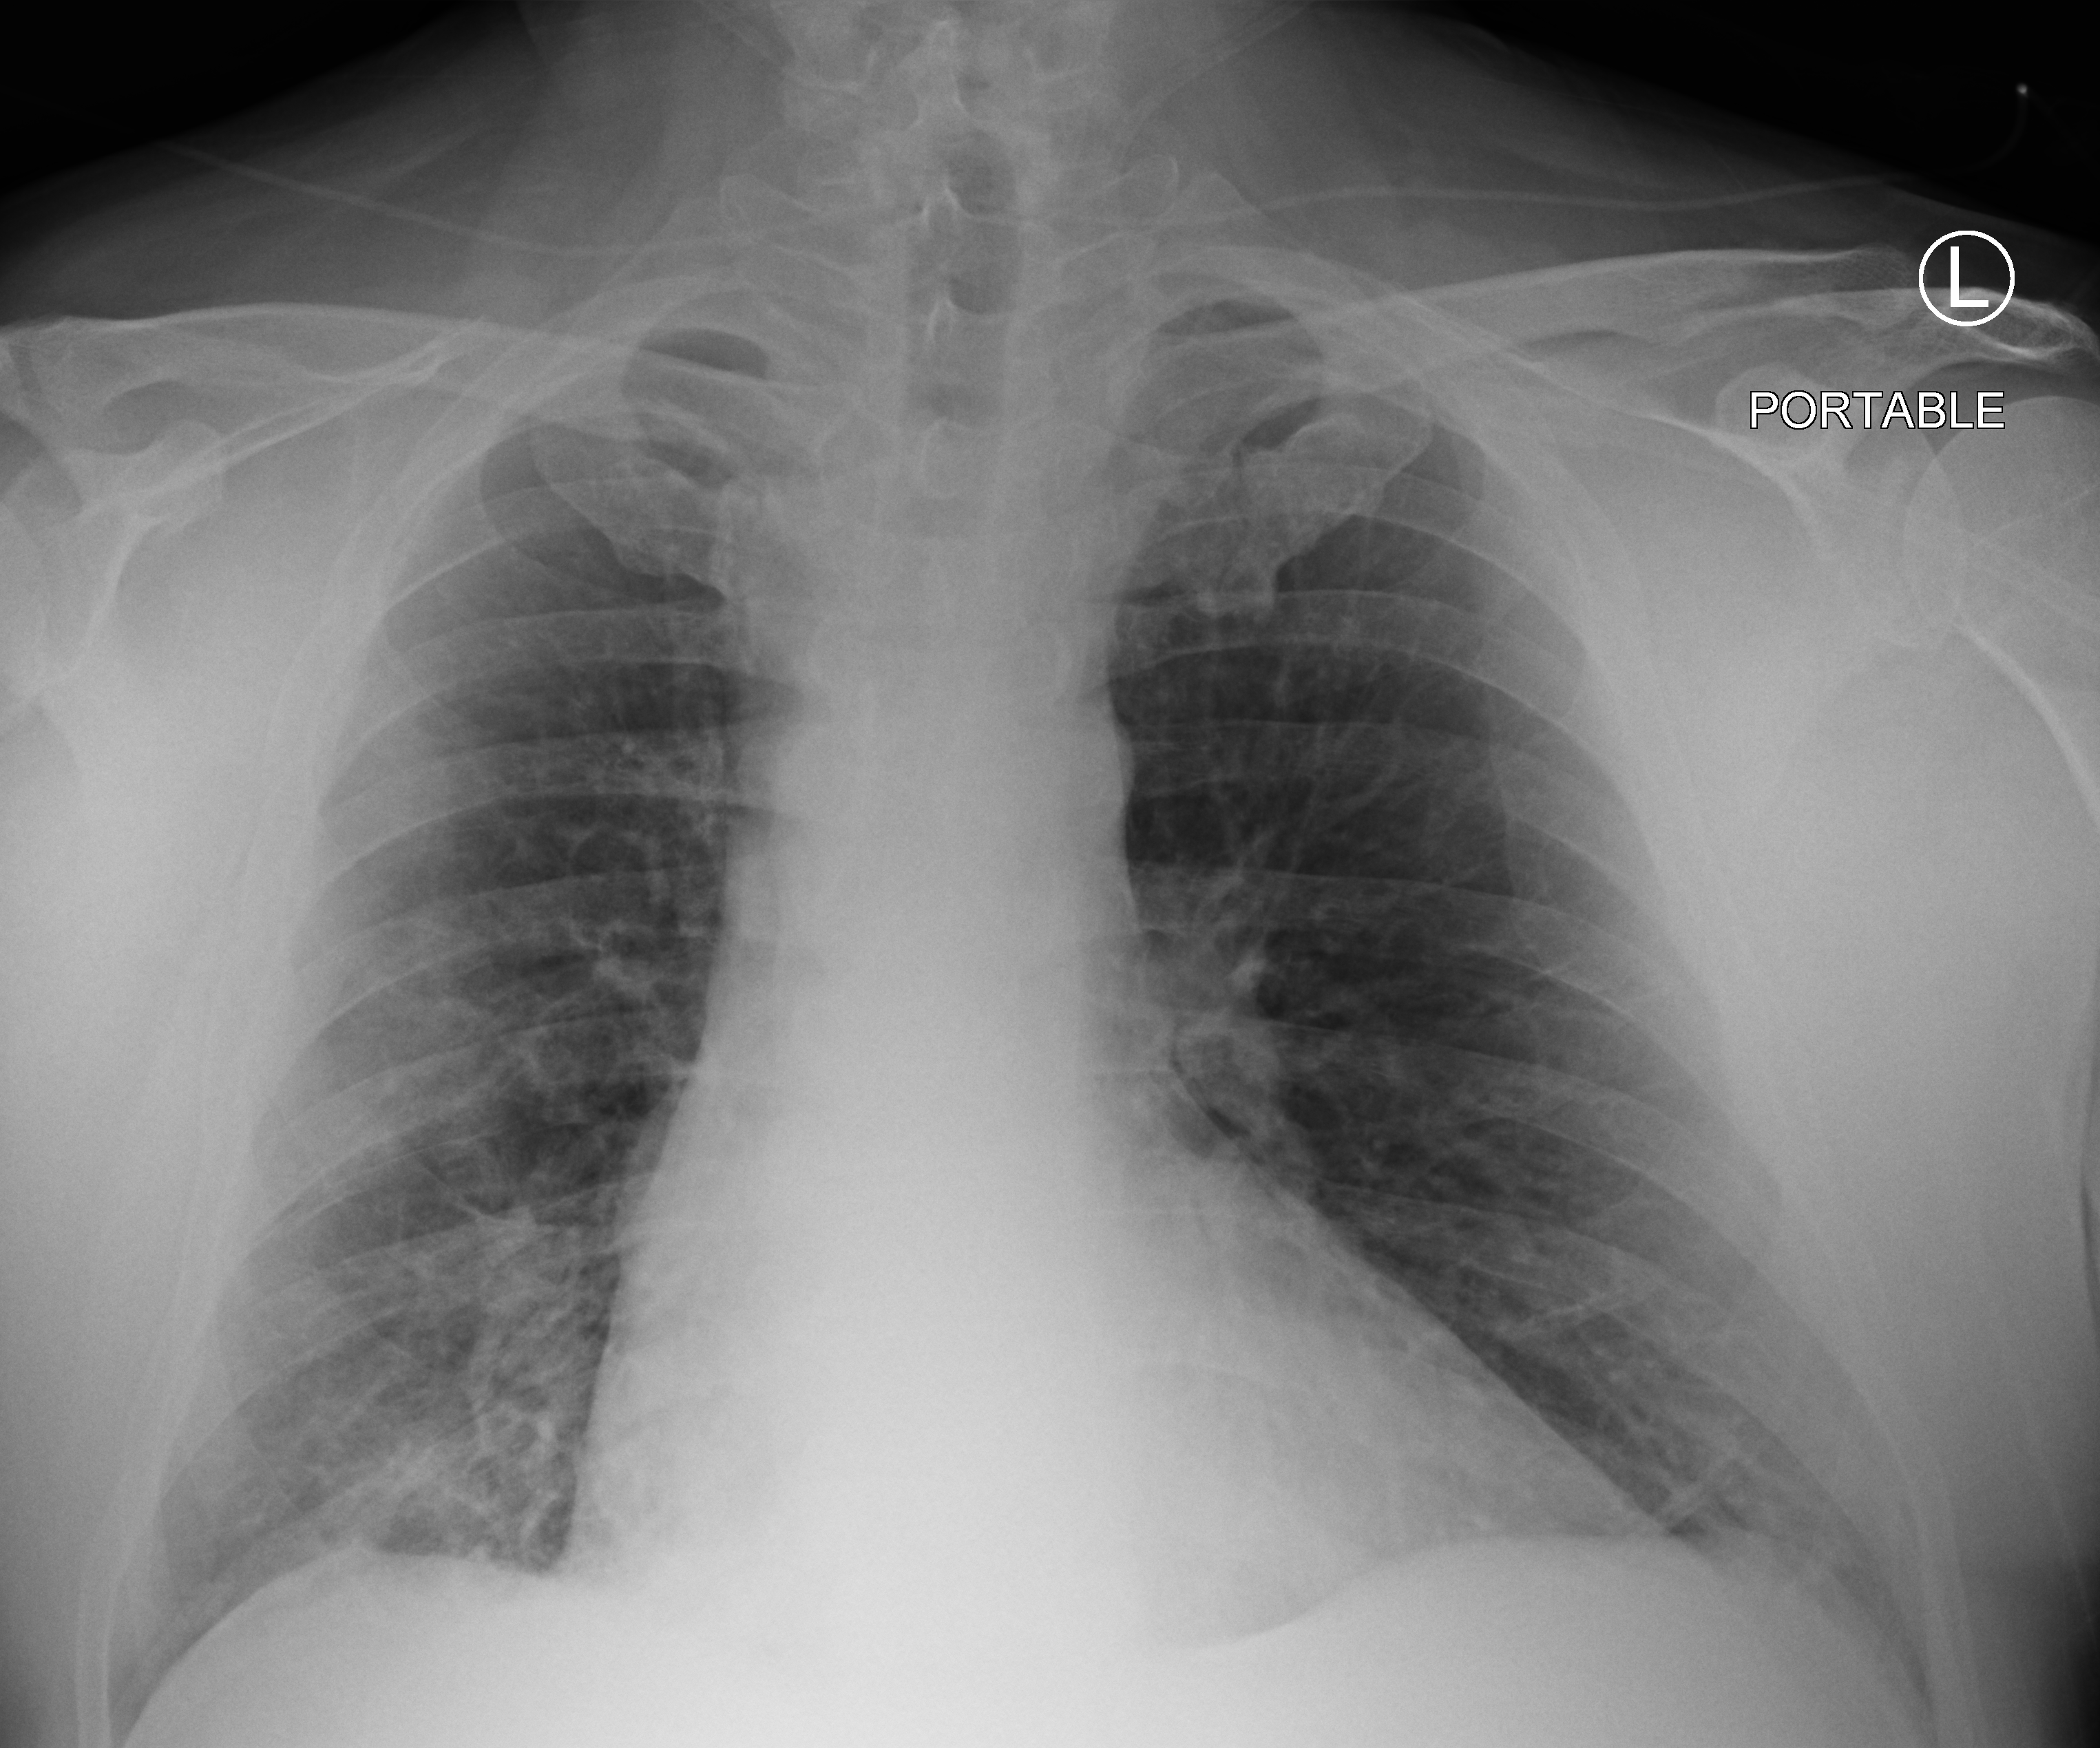
Chest X-ray (portable), anteroposterior (AP) projection. Male patient hospitalised with COVID-19, age 18–59 years.
Hospital-stay facts (about this admission, not read from this image; timing relative to this image not recorded): chronic kidney disease (admission record): no; other chronic lung disease (admission record): no.